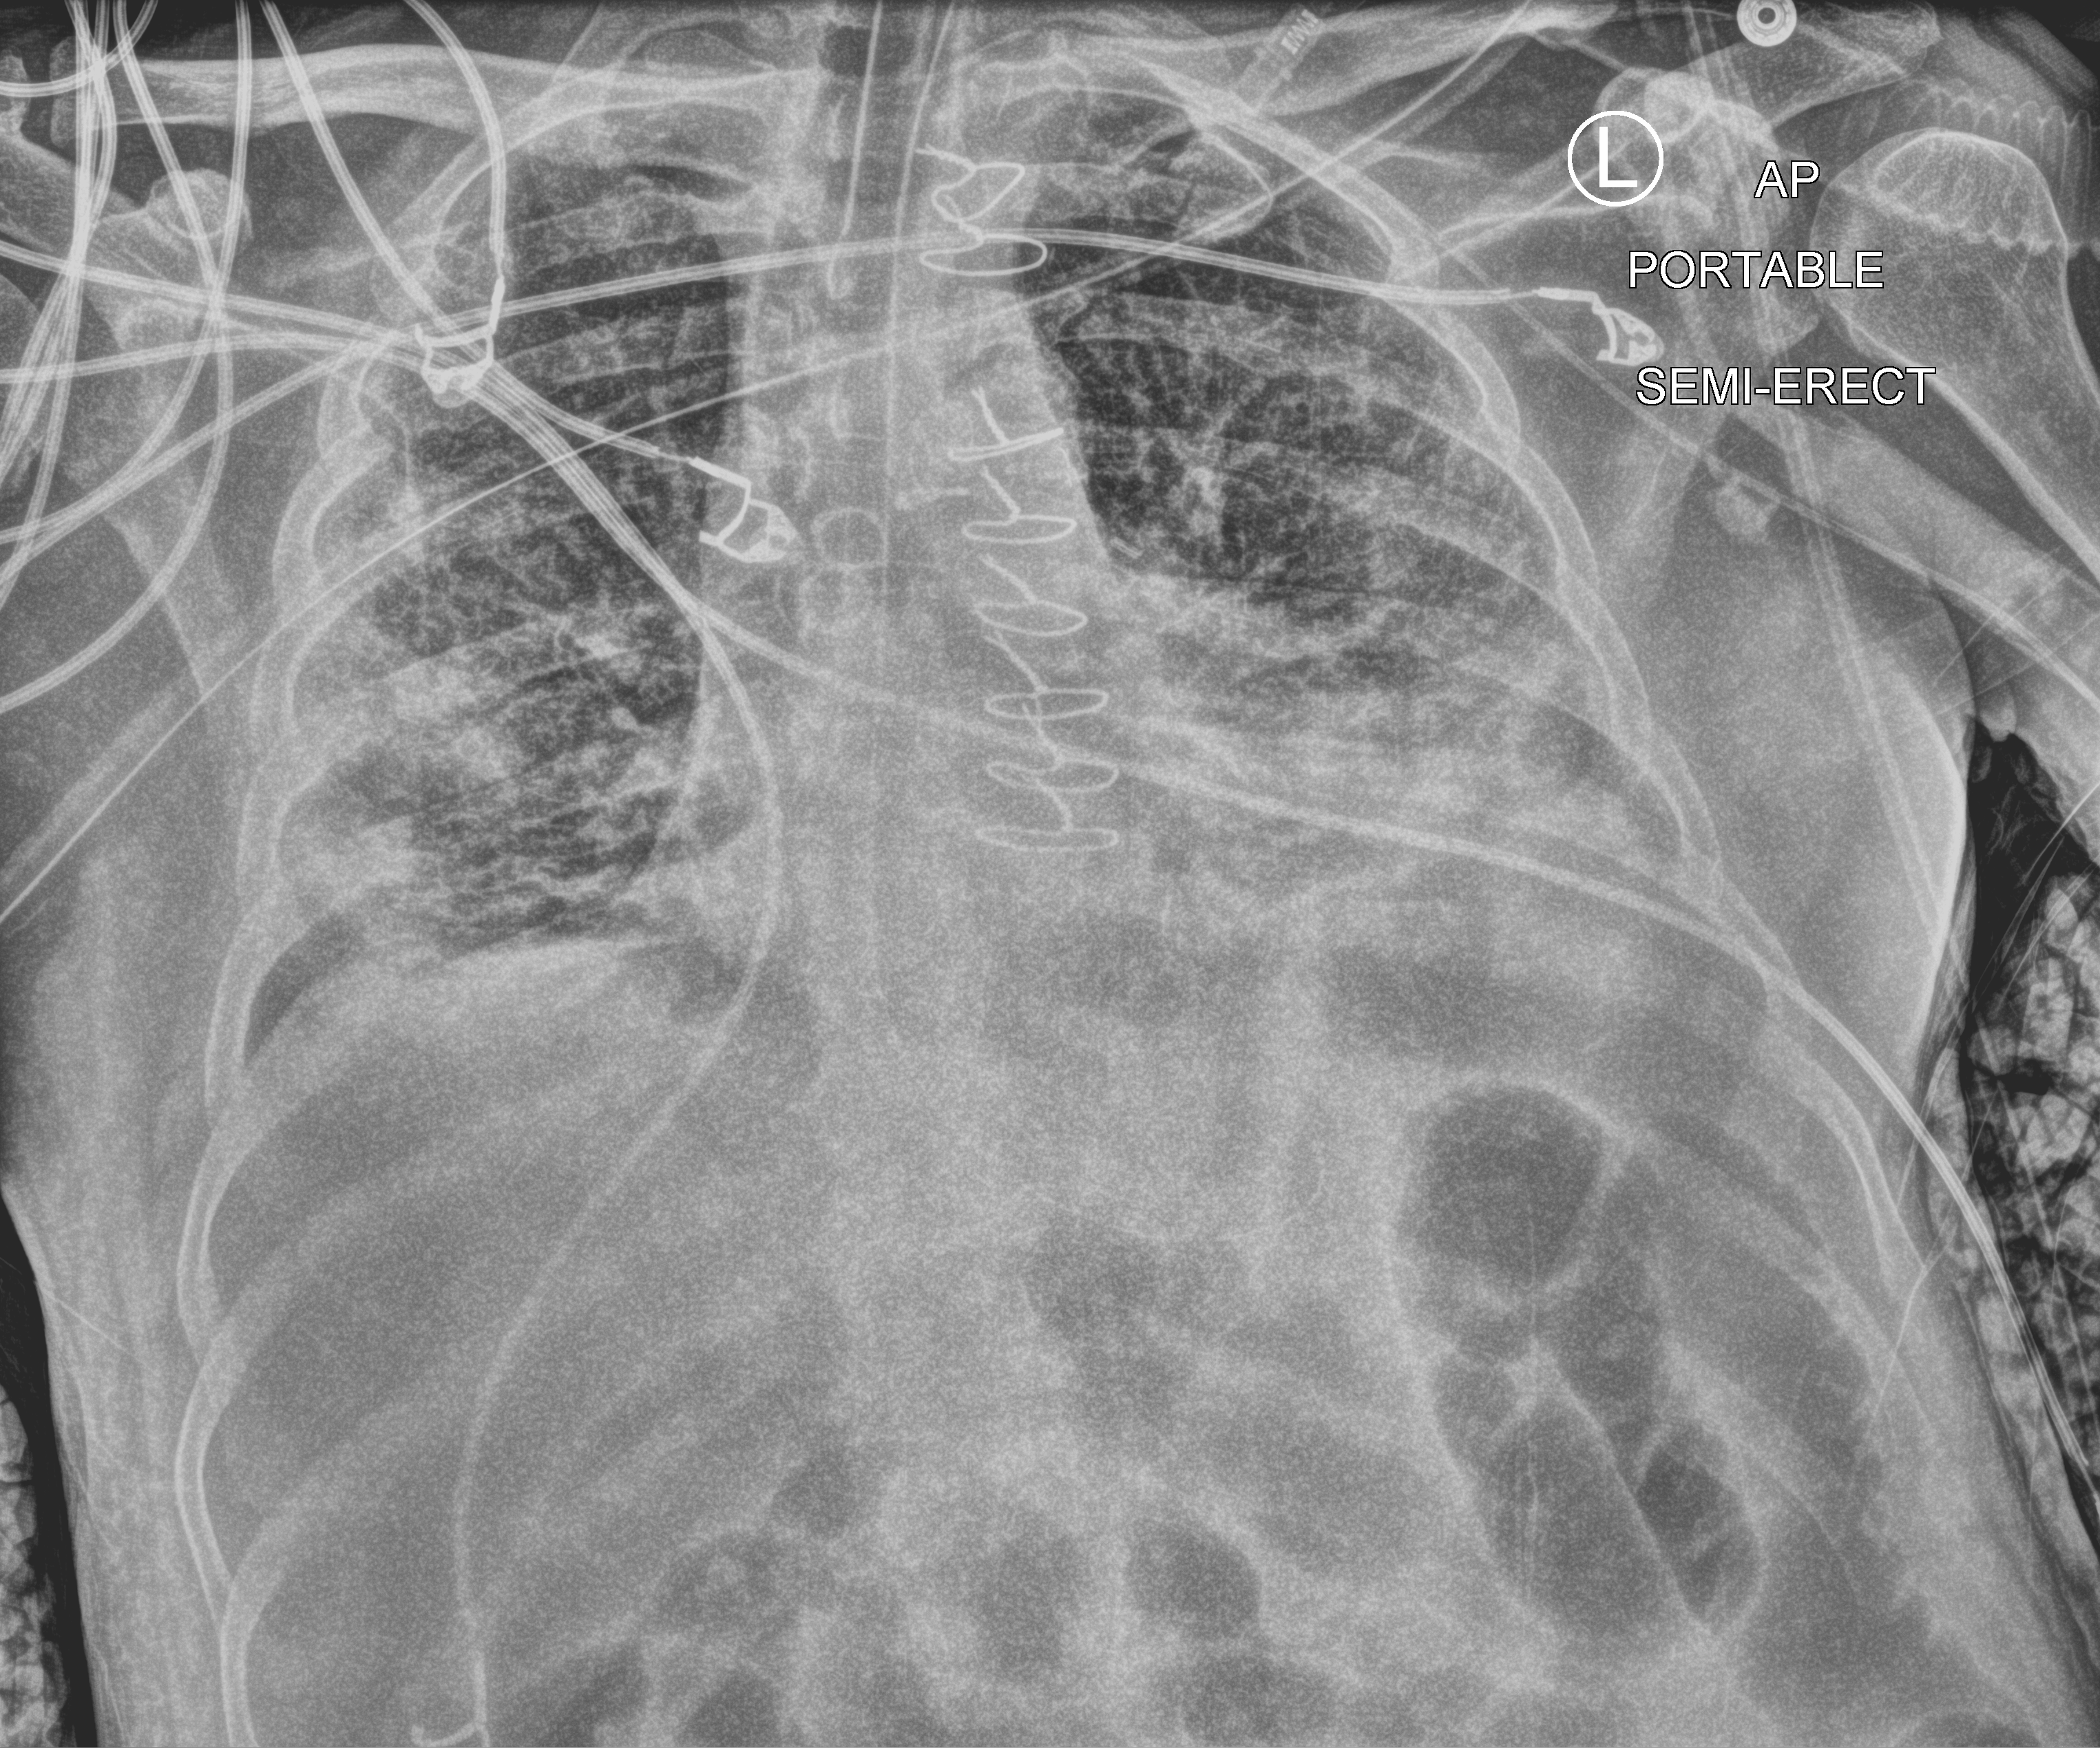
Portable chest radiograph, anteroposterior (AP) projection. Patient hospitalised with COVID-19; male, aged 18–59 years.
Admission-level facts for this patient (not findings on this image; timing relative to this image not recorded):
- admitted to intensive care during this hospital stay: yes
- diabetes (admission record): yes
- other chronic lung disease (admission record): yes